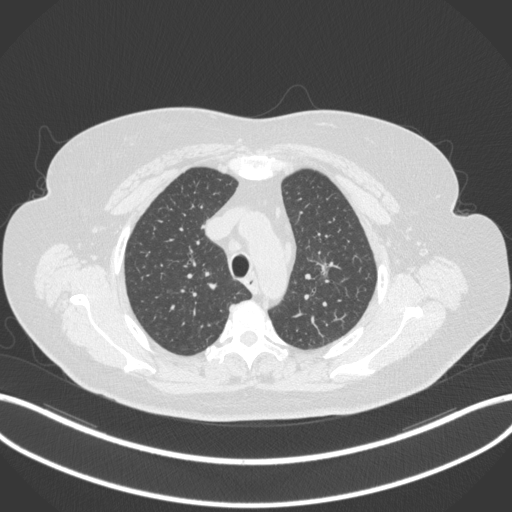
Chest CT, one axial slice; position 258 of 310 along the scan axis; lung window (W 1500 / L -600 HU); 512 × 512 image matrix, field of view 400 × 400 mm. Patient: female, 70 years. From the clinical record (not read from this slice): clinical TNM (as recorded): T1c N0 M0.
Outlined on this slice (bounding box drawn by a radiologist):
- lung tumour (recorded histology: adenocarcinoma): bounding box <315,254,339,284> (left, top, right, bottom; pixels)